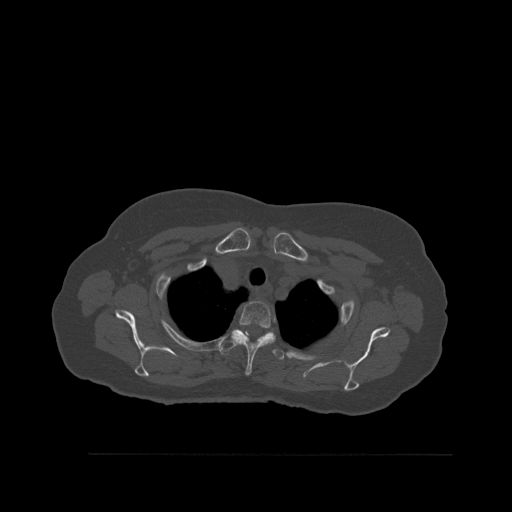
CT including the spine, one axial slice. Slice 428 of 527 in the series (ordered by position). Bone window (W 1800 / L 400 HU). 1.5 mm slice thickness. 512 × 512 image matrix, field of view 470 × 470 mm. Patient: female, 73 years. Case-level facts recorded for this patient, not image findings: primary cancer: breast.
Annotated regions visible in this slice (semi-automatically segmented with operator editing):
- T2 vertebra: box from (x=231, y=301) to (x=274, y=376) px
- T3 vertebra: (x=219, y=334)–(x=287, y=360)